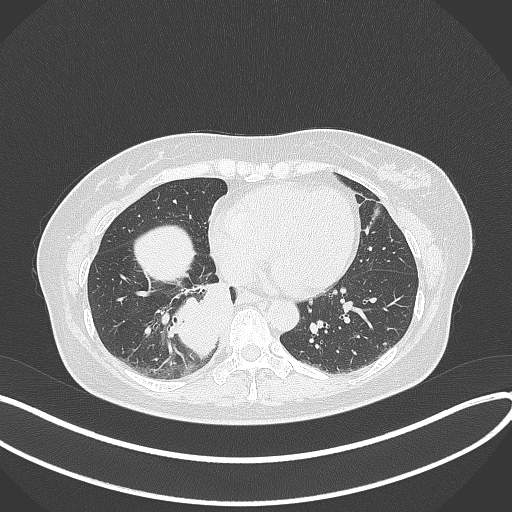
Chest CT, one axial slice. Position 122 of 331 along the scan axis. Reconstruction kernel B70f. 120 kVp. Lung window (W 1500 / L -600 HU). 1 mm slice thickness. 512 × 512 image matrix. Female patient, age 54 years. Case-level facts recorded for this patient, not image findings: clinical TNM (as recorded): T4 N0 M0.
Structures marked on this image (rectangle marked by the reading radiologist):
- lung tumour (recorded histology: adenocarcinoma): bounding box (x1, y1, x2, y2) in pixels: (163, 282, 238, 360)